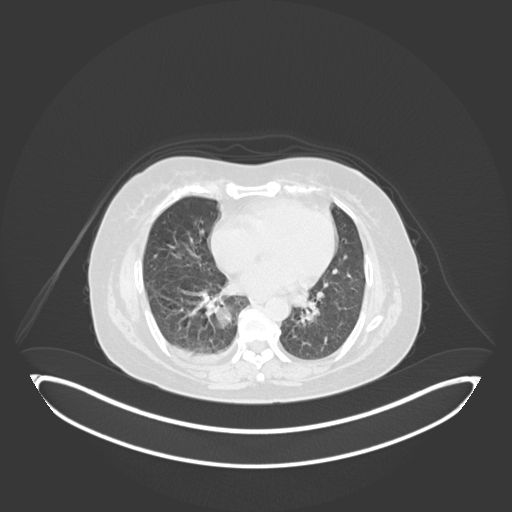
Chest CT, one axial slice; slice 64 of 231 in the series (ordered by position); reconstruction kernel B30f; 120 kVp; lung window (W 1500 / L -600 HU); 1 mm slice thickness; 512 × 512 image matrix. Patient: female, 56 years. Case-level facts recorded for this patient, not image findings: clinical TNM (as recorded): T2b N1 M0.
Annotated regions visible in this slice (bounding box drawn by a radiologist):
- lung tumour (recorded histology: small cell carcinoma): bounding box <215,298,237,332> (left, top, right, bottom; pixels)